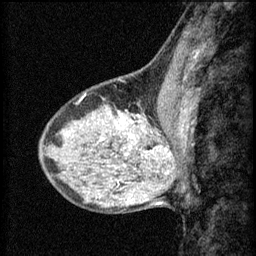
Breast MRI (dynamic contrast-enhanced), one sagittal slice. Slice 22 of 60 in the series (ordered by position). 3 images stored at this slice position (order not interpretable as contrast timing). 1.5 T. TE 4.2 ms, TR 8.2 ms. 256 × 256 image matrix. Patient: female, 40 years.
Outlined on this slice (semi-automatically segmented with operator editing):
- analysis volume of interest (the breast-tissue region the enhancement analysis was run in; not a lesion): box from (x=108, y=108) to (x=167, y=159) px
- tumour enhancement mask (voxels above the 70 % enhancement threshold inside the analysis volume of interest): (x=120, y=114)–(x=167, y=151)